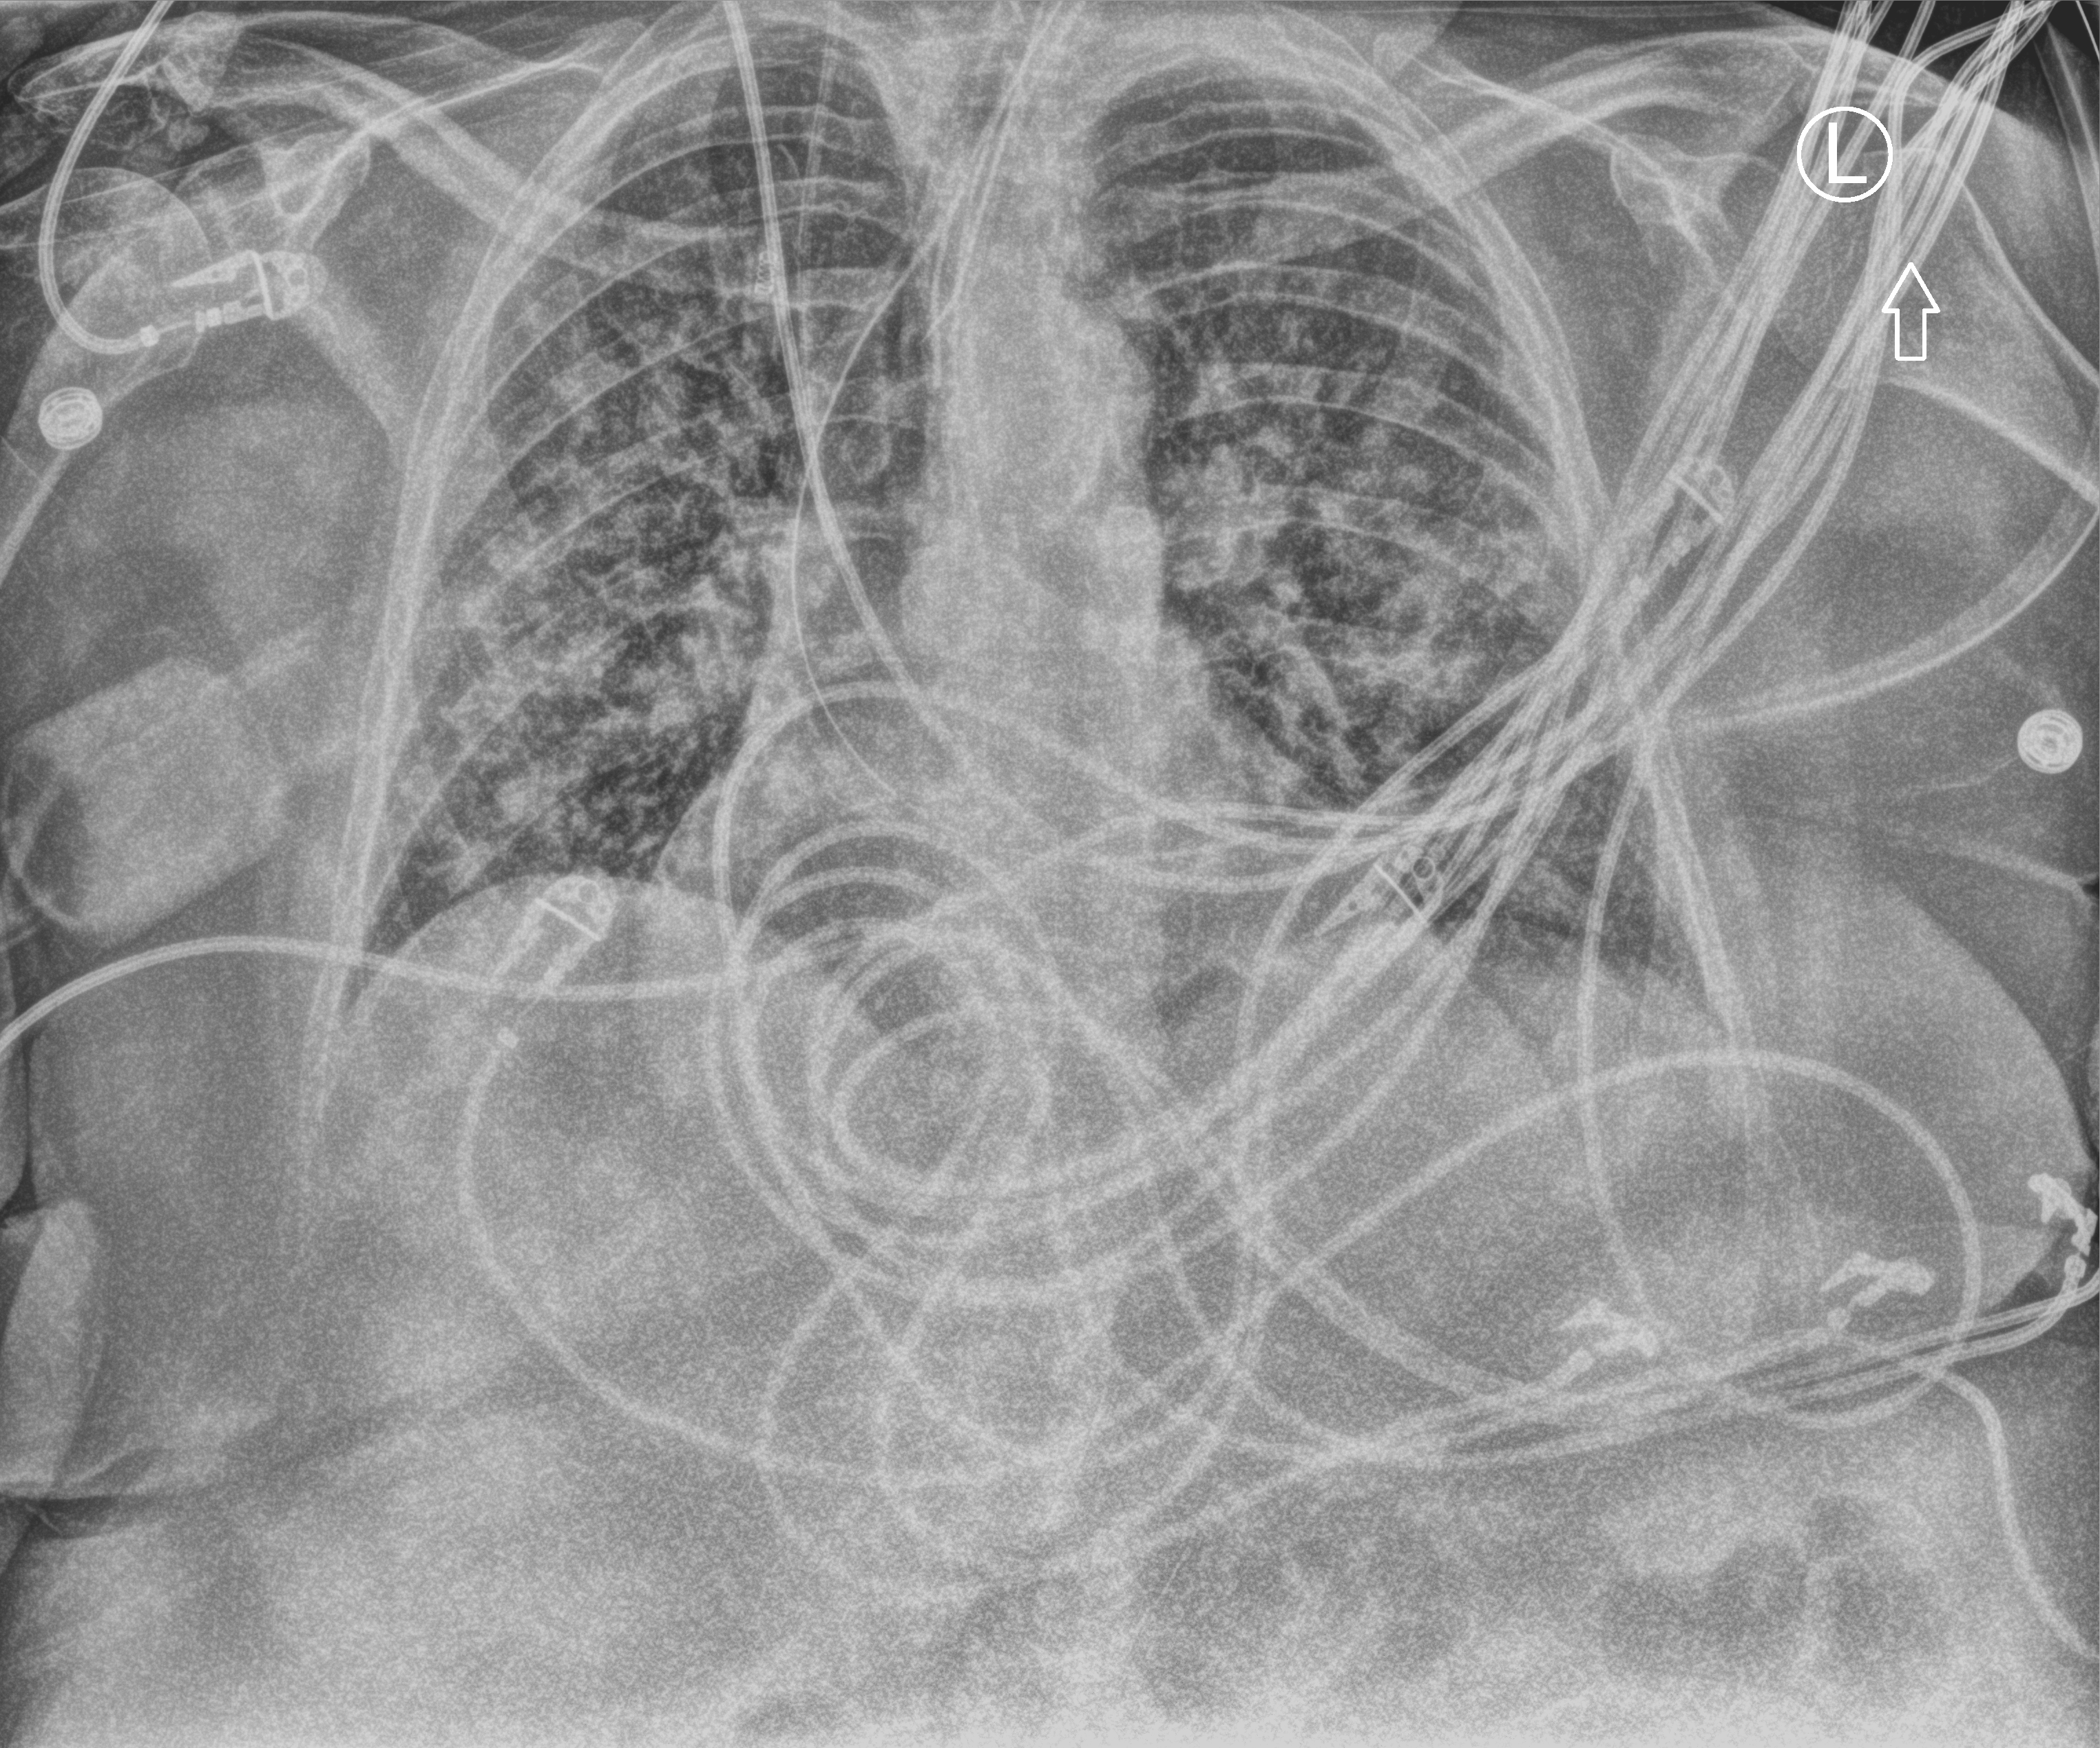
Bedside chest radiograph (computed radiography), anteroposterior (AP) projection. Female patient hospitalised with COVID-19, age 75–90 years.
From the hospital-stay record, not from the radiograph (when in the stay this image was taken is not recorded): mechanically ventilated during this hospital stay: yes.